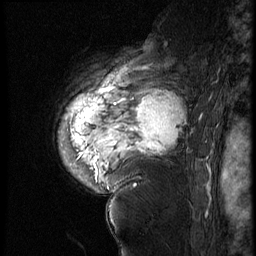
Breast MRI (dynamic contrast-enhanced), one sagittal slice; slice 47 of 60 in the series (ordered by position); 4 images stored at this slice position (order not interpretable as contrast timing); 1.5 T; TE 4.2 ms, TR 9 ms; 2.5 mm slice thickness; 256 × 256 image matrix, field of view 180 × 180 mm. Female patient, age 56 years. Case-level facts recorded for this patient, not image findings: setting: breast cancer imaged before/during neoadjuvant chemotherapy; receptor status: HER2-positive.
Outlined on this slice (semi-automatically segmented with operator editing):
- analysis volume of interest (the breast-tissue region the enhancement analysis was run in; not a lesion): bounding box <82,83,199,177> (left, top, right, bottom; pixels)
- tumour enhancement mask (voxels above the 140 % enhancement threshold inside the analysis volume of interest): <113,96,183,154>